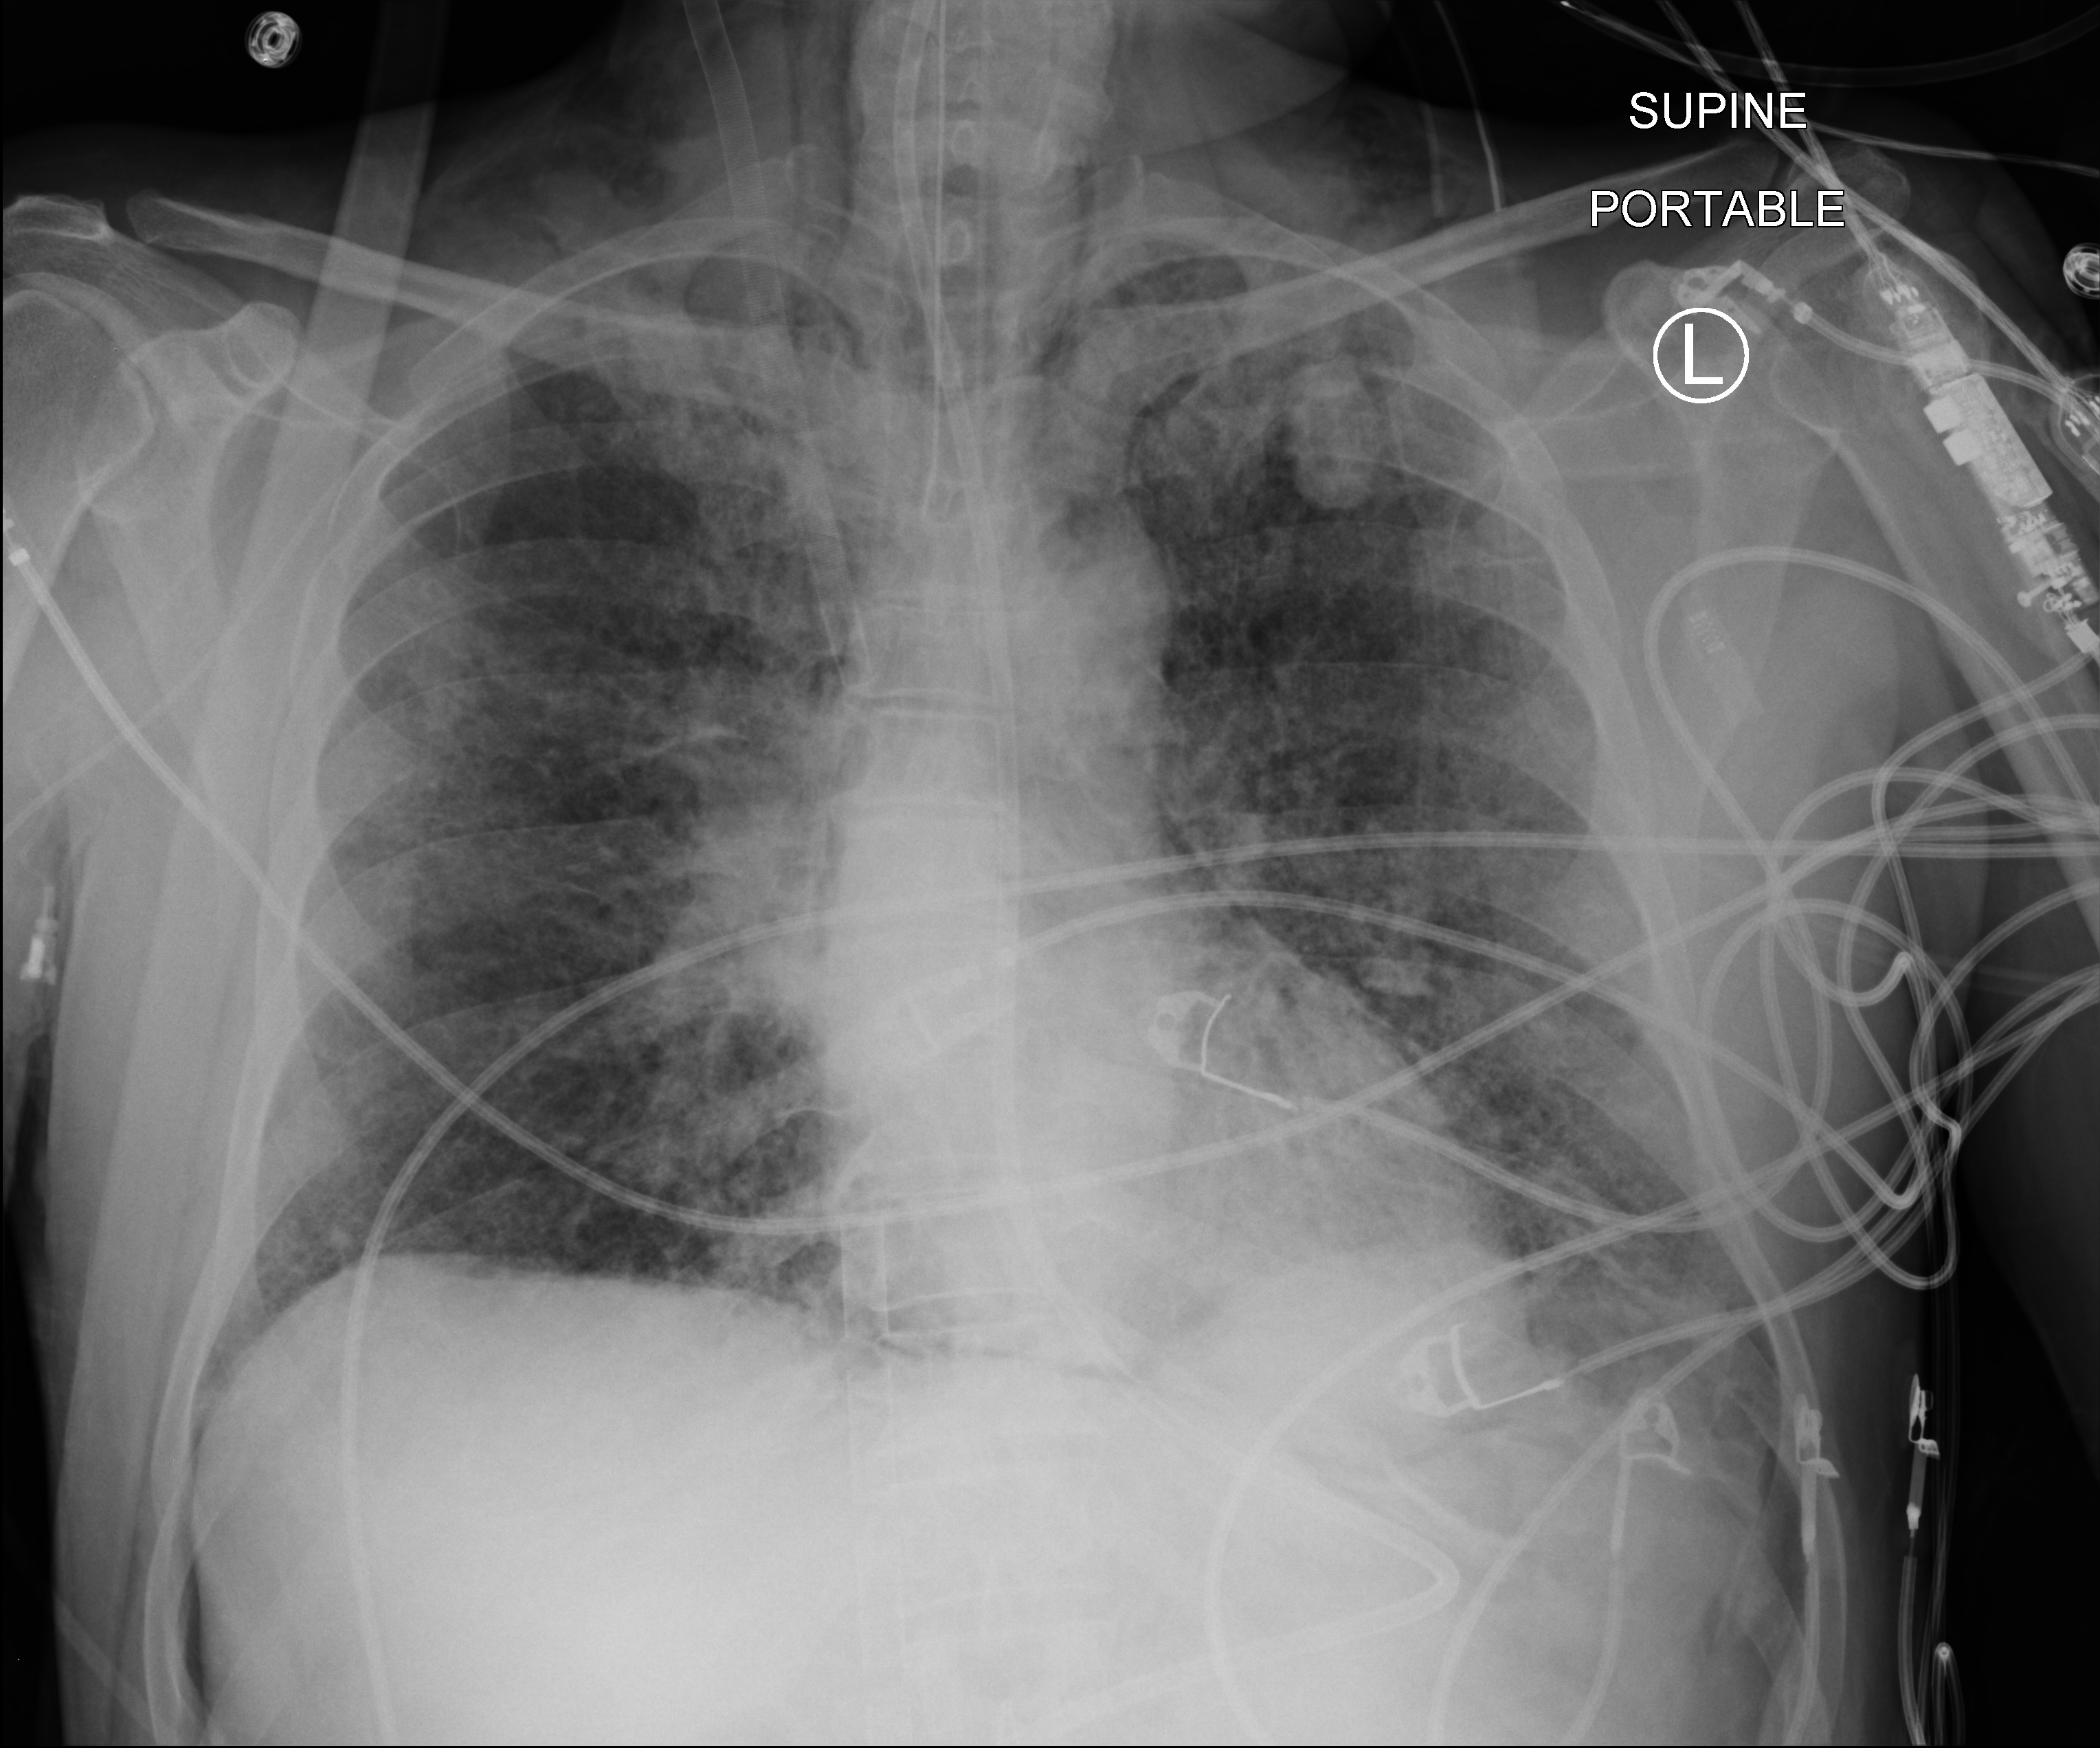
Chest X-ray (portable); anteroposterior (AP) projection. Patient hospitalised with COVID-19; male, aged 18–59 years.
Hospital-stay facts (about this admission, not read from this image; timing relative to this image not recorded):
- mechanically ventilated during this hospital stay: yes
- admitted to intensive care during this hospital stay: yes